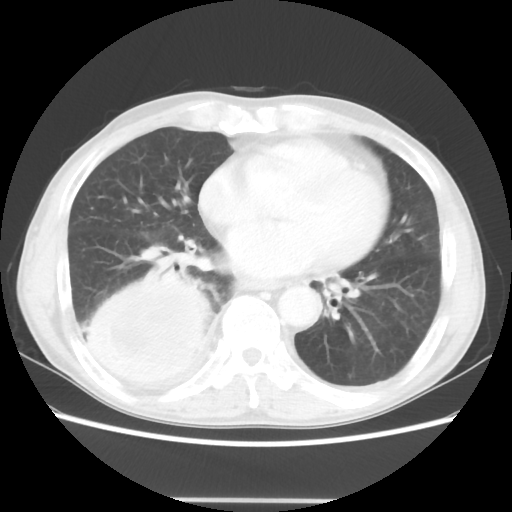
Chest CT, one axial slice; slice 17 of 48 in the series (ordered by position); lung window (W 1500 / L -600 HU); 512 × 512 image matrix. Male patient, age 66 years. Case-level facts recorded for this patient, not image findings: clinical TNM (as recorded): T4 N1 M1; histopathological grade: G3.
Outlined on this slice (bounding box drawn by a radiologist):
- lung tumour (recorded histology: small cell carcinoma): bounding box <72,269,212,389> (left, top, right, bottom; pixels)